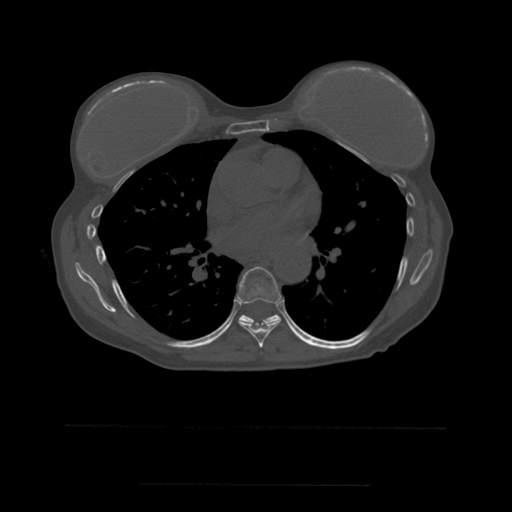
CT including the spine, one axial slice; slice 351 of 544 in the series (ordered by position); bone window (W 1800 / L 400 HU); 1.25 mm slice thickness; 512 × 512 image matrix, field of view 350 × 350 mm. Patient age 58 years. Case-level facts recorded for this patient, not image findings: primary cancer: lung.
Annotated regions visible in this slice (semi-automatically segmented with operator editing):
- T7 vertebra: bounding box [x1, y1, x2, y2] px = [236, 267, 282, 348]
- T8 vertebra: [239, 315, 281, 329]